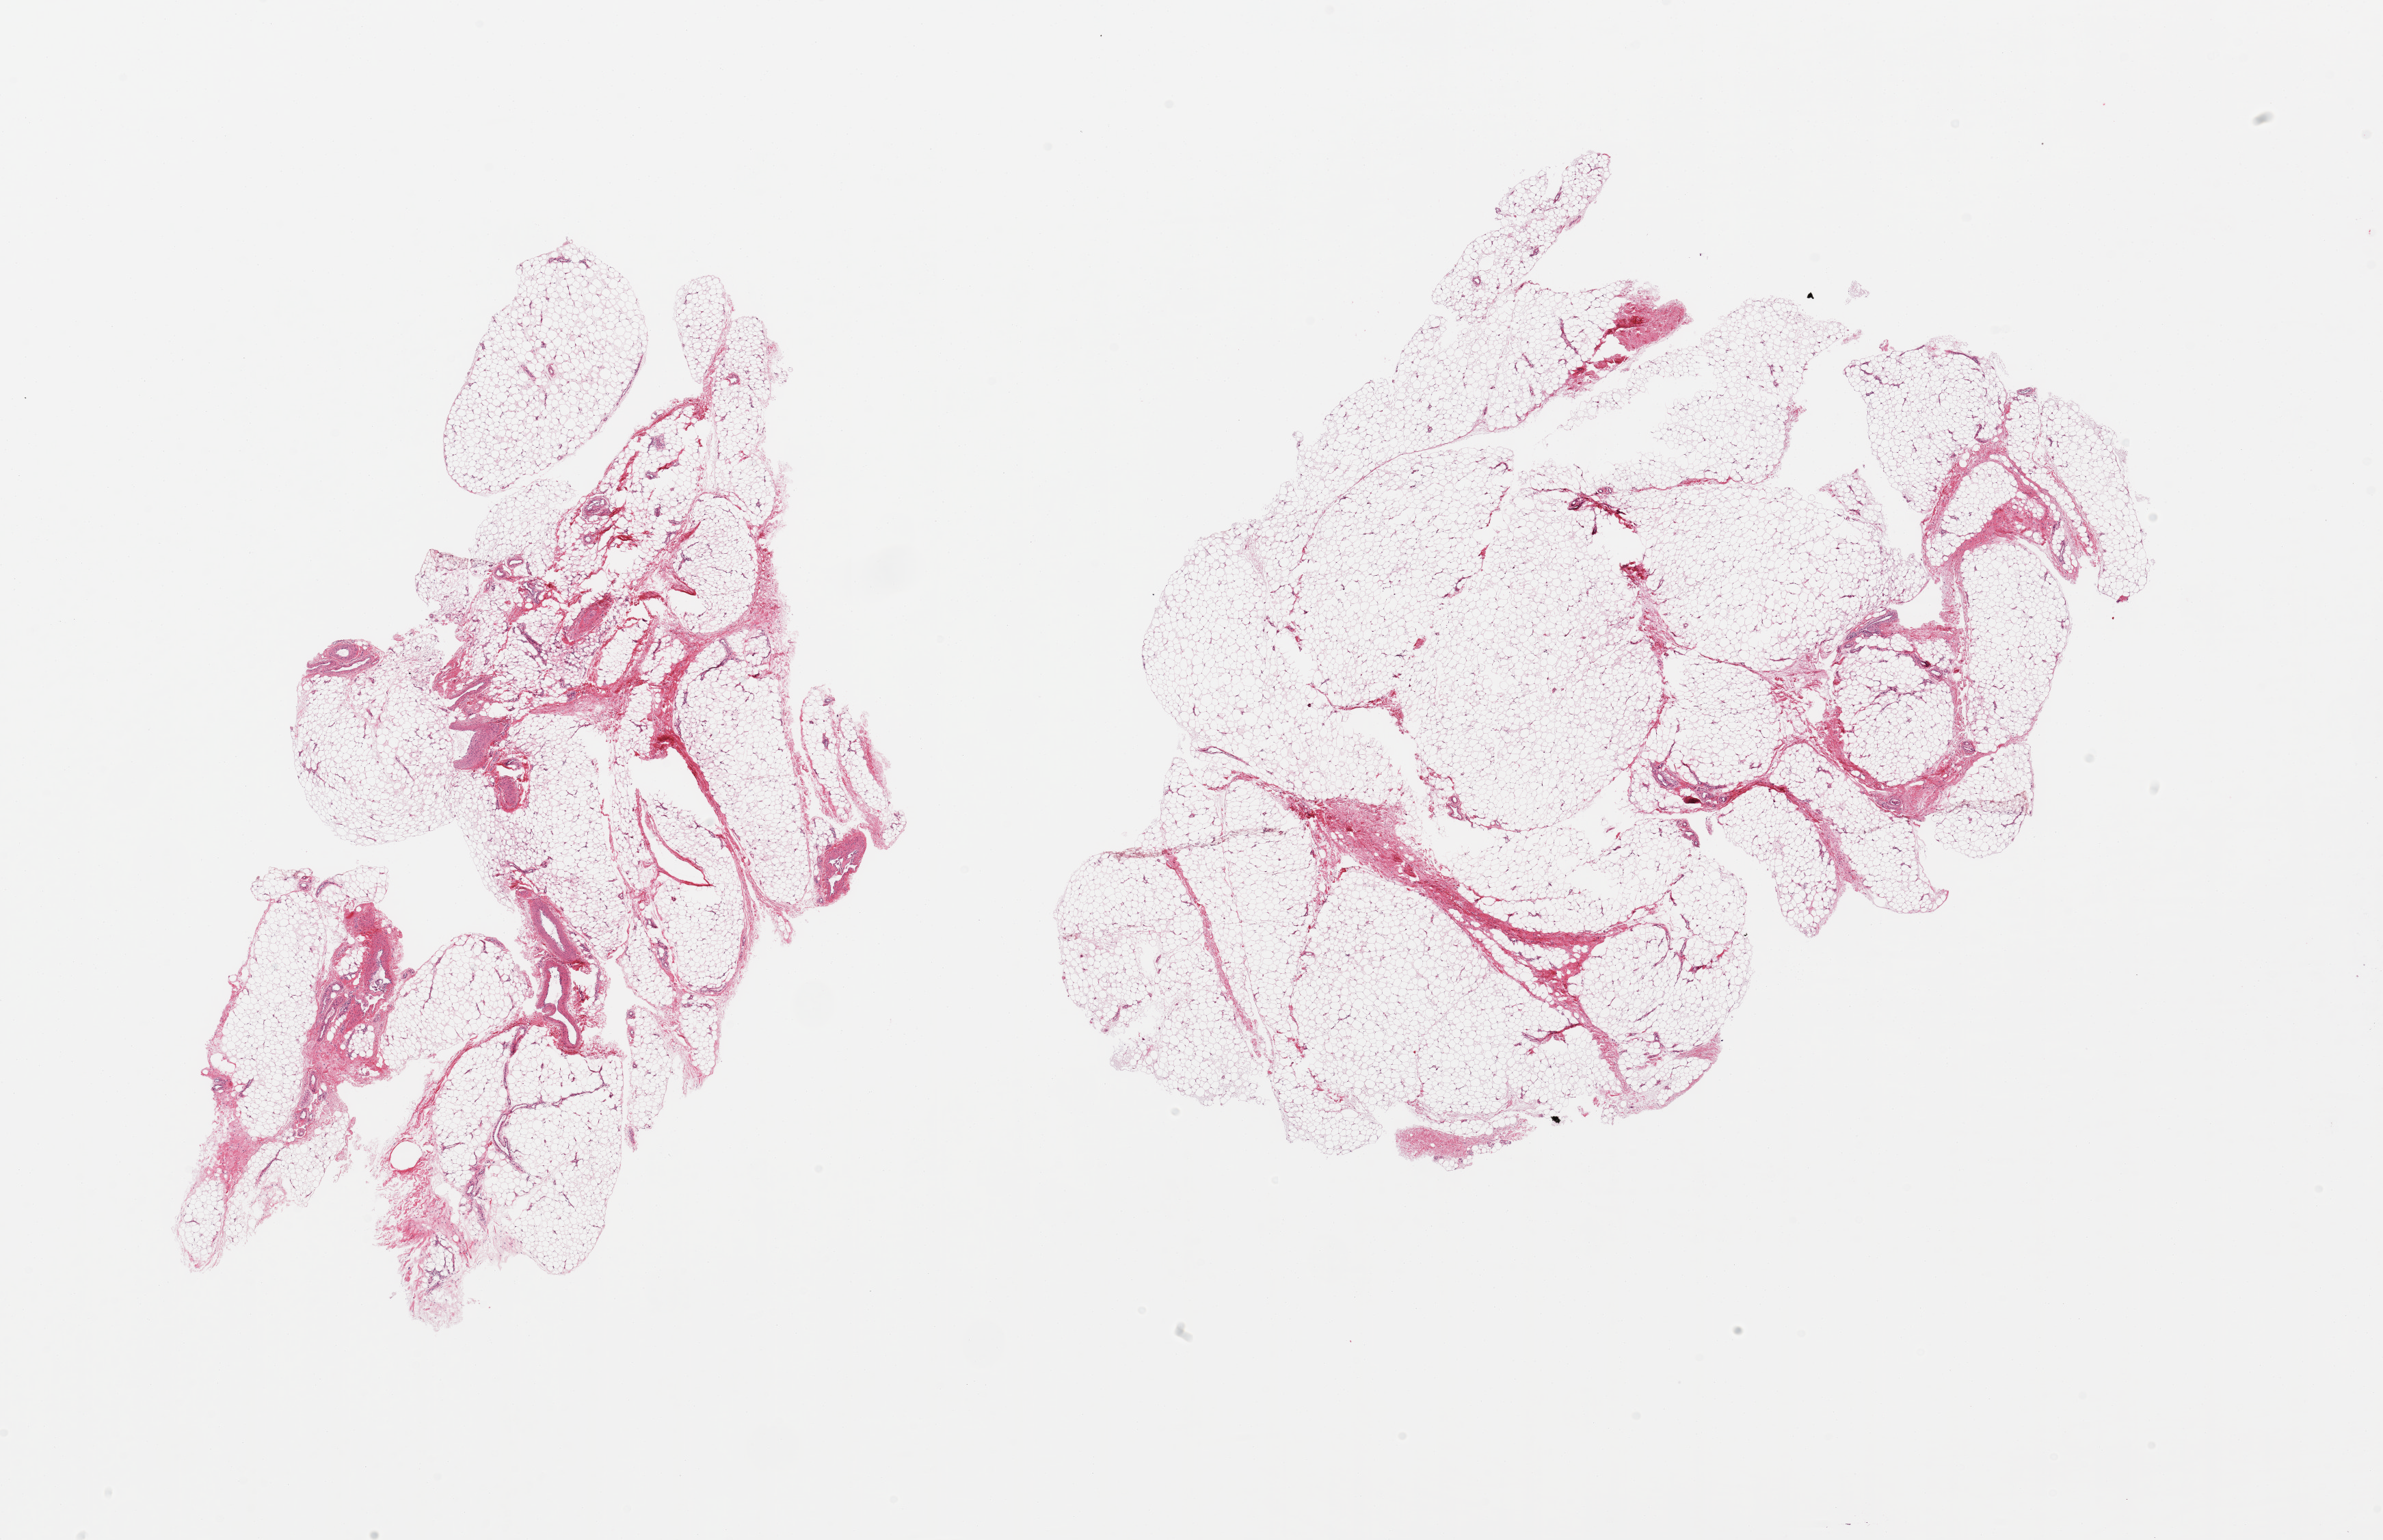
Whole-slide image, hematoxylin and eosin (H&E) stain — low-resolution overview of the scanned area, about 27.6 x 17.8 mm (slide scanned at 20x). PAXgene-fixed, paraffin-embedded tissue. Section of adipose tissue (target tissue). Donor tissue sample.
Reviewer comment on this tissue sample: 2 pieces, fascia/vascular elements are ~10-15% of tissue.